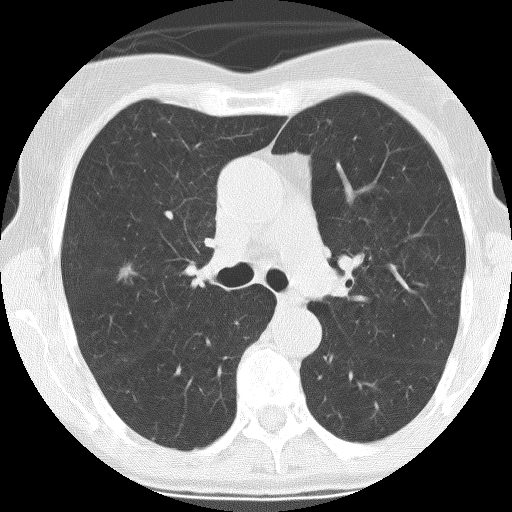
Axial slice from a low-dose chest CT screening exam. Baseline screening round. Lung window (W 1500 / L -600 HU). 2.5 mm slice thickness. Lung (sharp) reconstruction kernel (BONE). 120 kVp. Slice 93 of 261 in the series. Female participant, aged 68 years at enrolment. Former smoker at enrolment.
• Lesion marked by an expert reader, bounding box [x1, y1, x2, y2] px = [104, 249, 146, 293].
• Reader record for this screening exam (exam-level; its link to the box is not recorded): non-calcified nodule or mass ≥4 mm, right upper lobe, 13 × 8 mm, spiculated (stellate) margins, mixed attenuation.
• Official screen result: positive, change unspecified: nodule(s) >= 4 mm or enlarging nodule(s), mass(es), or other non-specific abnormalities suspicious for lung cancer.
• Lung cancer was diagnosed 113 days after this screen: adenocarcinoma, NOS, right upper lobe, moderately differentiated (G2), stage IA (AJCC 6th edition), 10 mm at pathology.